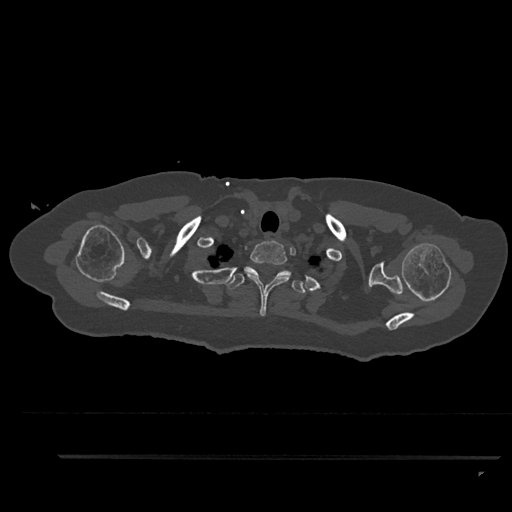
CT including the spine, one axial slice. Slice 746 of 797 in the series (ordered by position). 120 kVp. Bone window (W 1800 / L 400 HU). 0.5 mm slice thickness. 512 × 512 image matrix, field of view 408 × 408 mm. Patient: female, 44 years. From the clinical record (not read from this slice): primary cancer: renal.
Structures marked on this image (semi-automatically segmented with operator editing):
- T1 vertebra: bounding box [x1, y1, x2, y2] px = [243, 240, 291, 316]
- T2 vertebra: [226, 267, 306, 293]